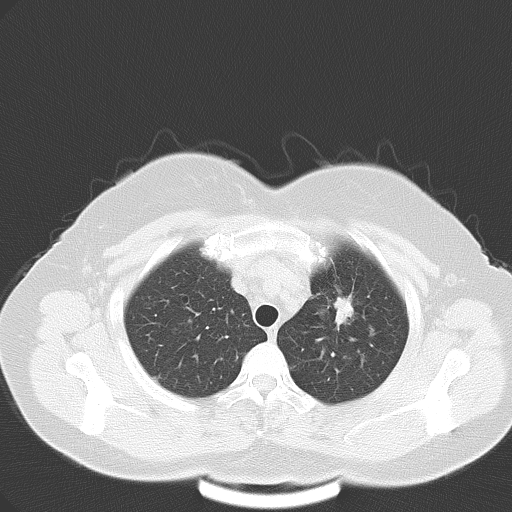
Chest CT, one axial slice; slice 45 of 57 in the series (ordered by position); reconstruction kernel B70f; 120 kVp; lung window (W 1500 / L -600 HU); 5 mm slice thickness; 512 × 512 image matrix, field of view 353 × 353 mm. Patient: female, 53 years. From the clinical record (not read from this slice): clinical TNM (as recorded): T1c N0 M1a.
Annotated regions visible in this slice (rectangle marked by the reading radiologist):
- lung tumour (recorded histology: adenocarcinoma): bounding box [x1, y1, x2, y2] px = [323, 292, 356, 329]